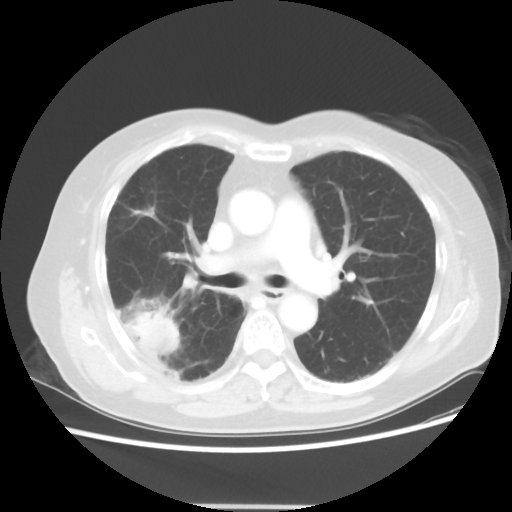
Chest CT, one axial slice; slice 29 of 50 in the series (ordered by position); reconstruction kernel STANDARD; 120 kVp; lung window (W 1500 / L -600 HU); 5 mm slice thickness; 512 × 512 image matrix, field of view 360 × 360 mm. Female patient, age 72 years. From the clinical record (not read from this slice): clinical TNM (as recorded): T2 N1 M0; histopathological grade: G1.
Outlined on this slice (bounding box drawn by a radiologist):
- lung tumour (recorded histology: adenocarcinoma): box from (x=123, y=309) to (x=178, y=360) px